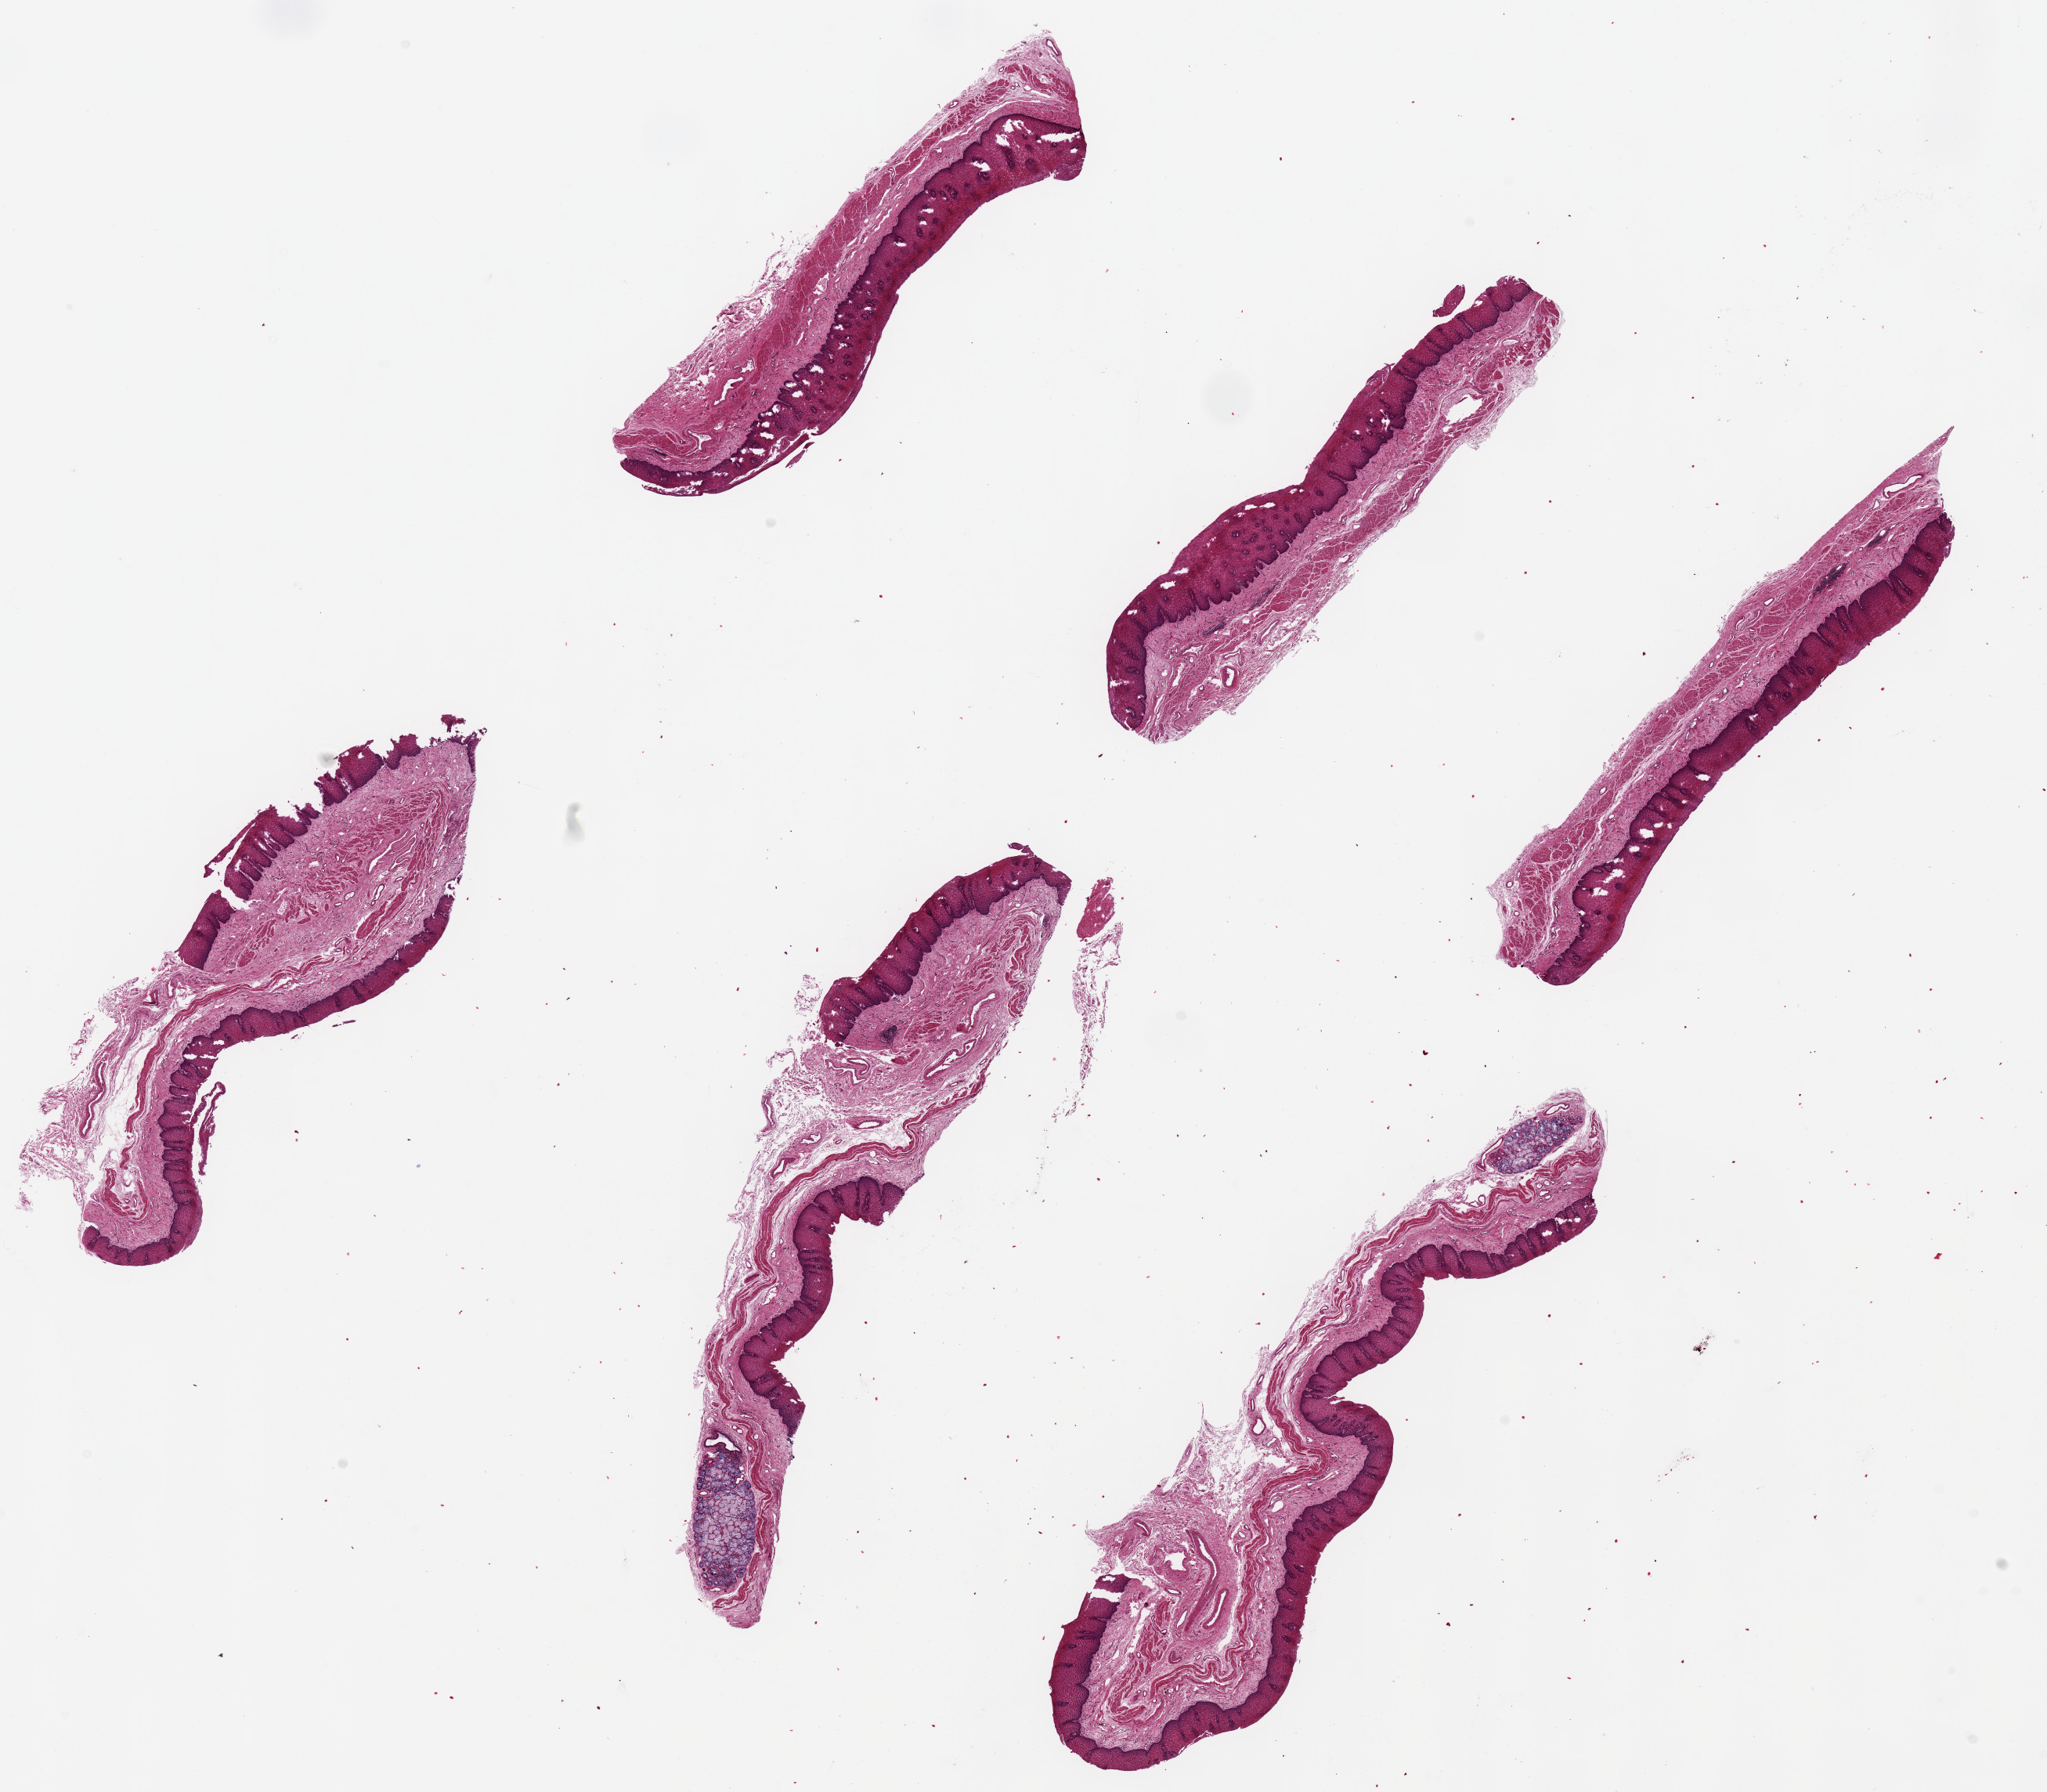
Whole-slide image, hematoxylin and eosin (H&E) stain, brightfield — low-resolution overview of the scanned area, about 20.7 x 18.1 mm (acquisition: 20x scan); PAXgene-fixed, paraffin-embedded tissue; section of esophageal mucous membrane (target tissue); donor tissue sample.
Reviewer comment on this tissue sample: 6 pieces up to 8.3x2.3 moderate tissue tears.